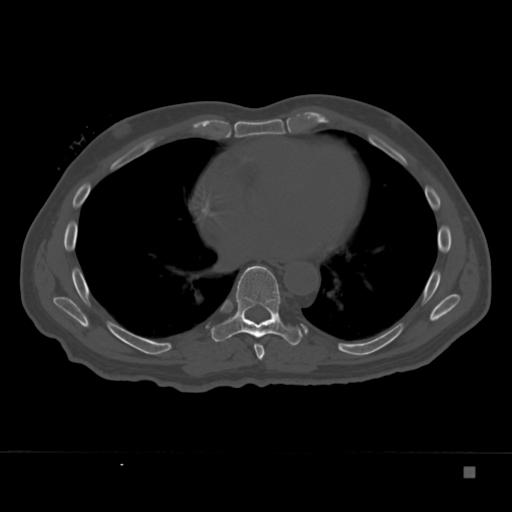
CT including the spine, one axial slice; slice 209 of 332 in the series (ordered by position); 120 kVp; bone window (W 1800 / L 400 HU); 1.5 mm slice thickness; 512 × 512 image matrix, field of view 389 × 389 mm. Male patient, age 72 years. Case-level facts recorded for this patient, not image findings: primary cancer: skeletal.
Outlined on this slice (semi-automatic segmentation, software-assisted and operator-edited):
- T7 vertebra: bounding box [x1, y1, x2, y2] px = [254, 343, 265, 360]
- T8 vertebra: [211, 265, 303, 346]